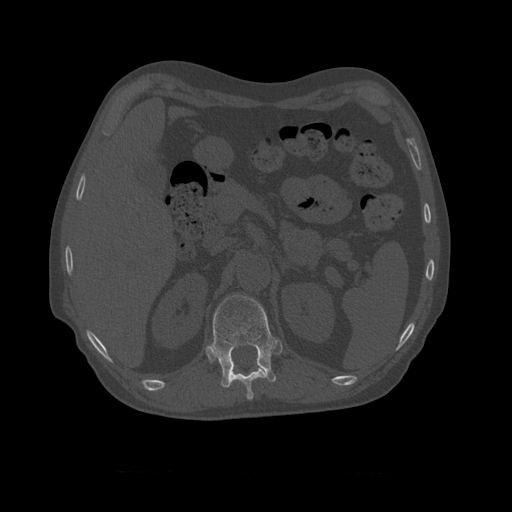
CT including the spine, one axial slice; position 385 of 450 along the scan axis; reconstruction kernel STANDARD; 120 kVp; bone window (W 1800 / L 400 HU); 512 × 512 image matrix, field of view 405 × 405 mm. Patient age 75 years. From the clinical record (not read from this slice): primary cancer: prostate.
Annotated regions visible in this slice (semi-automatic segmentation, software-assisted and operator-edited):
- T10 vertebra: box from (x=229, y=366) to (x=267, y=400) px
- T11 vertebra: (x=209, y=295)–(x=277, y=388)